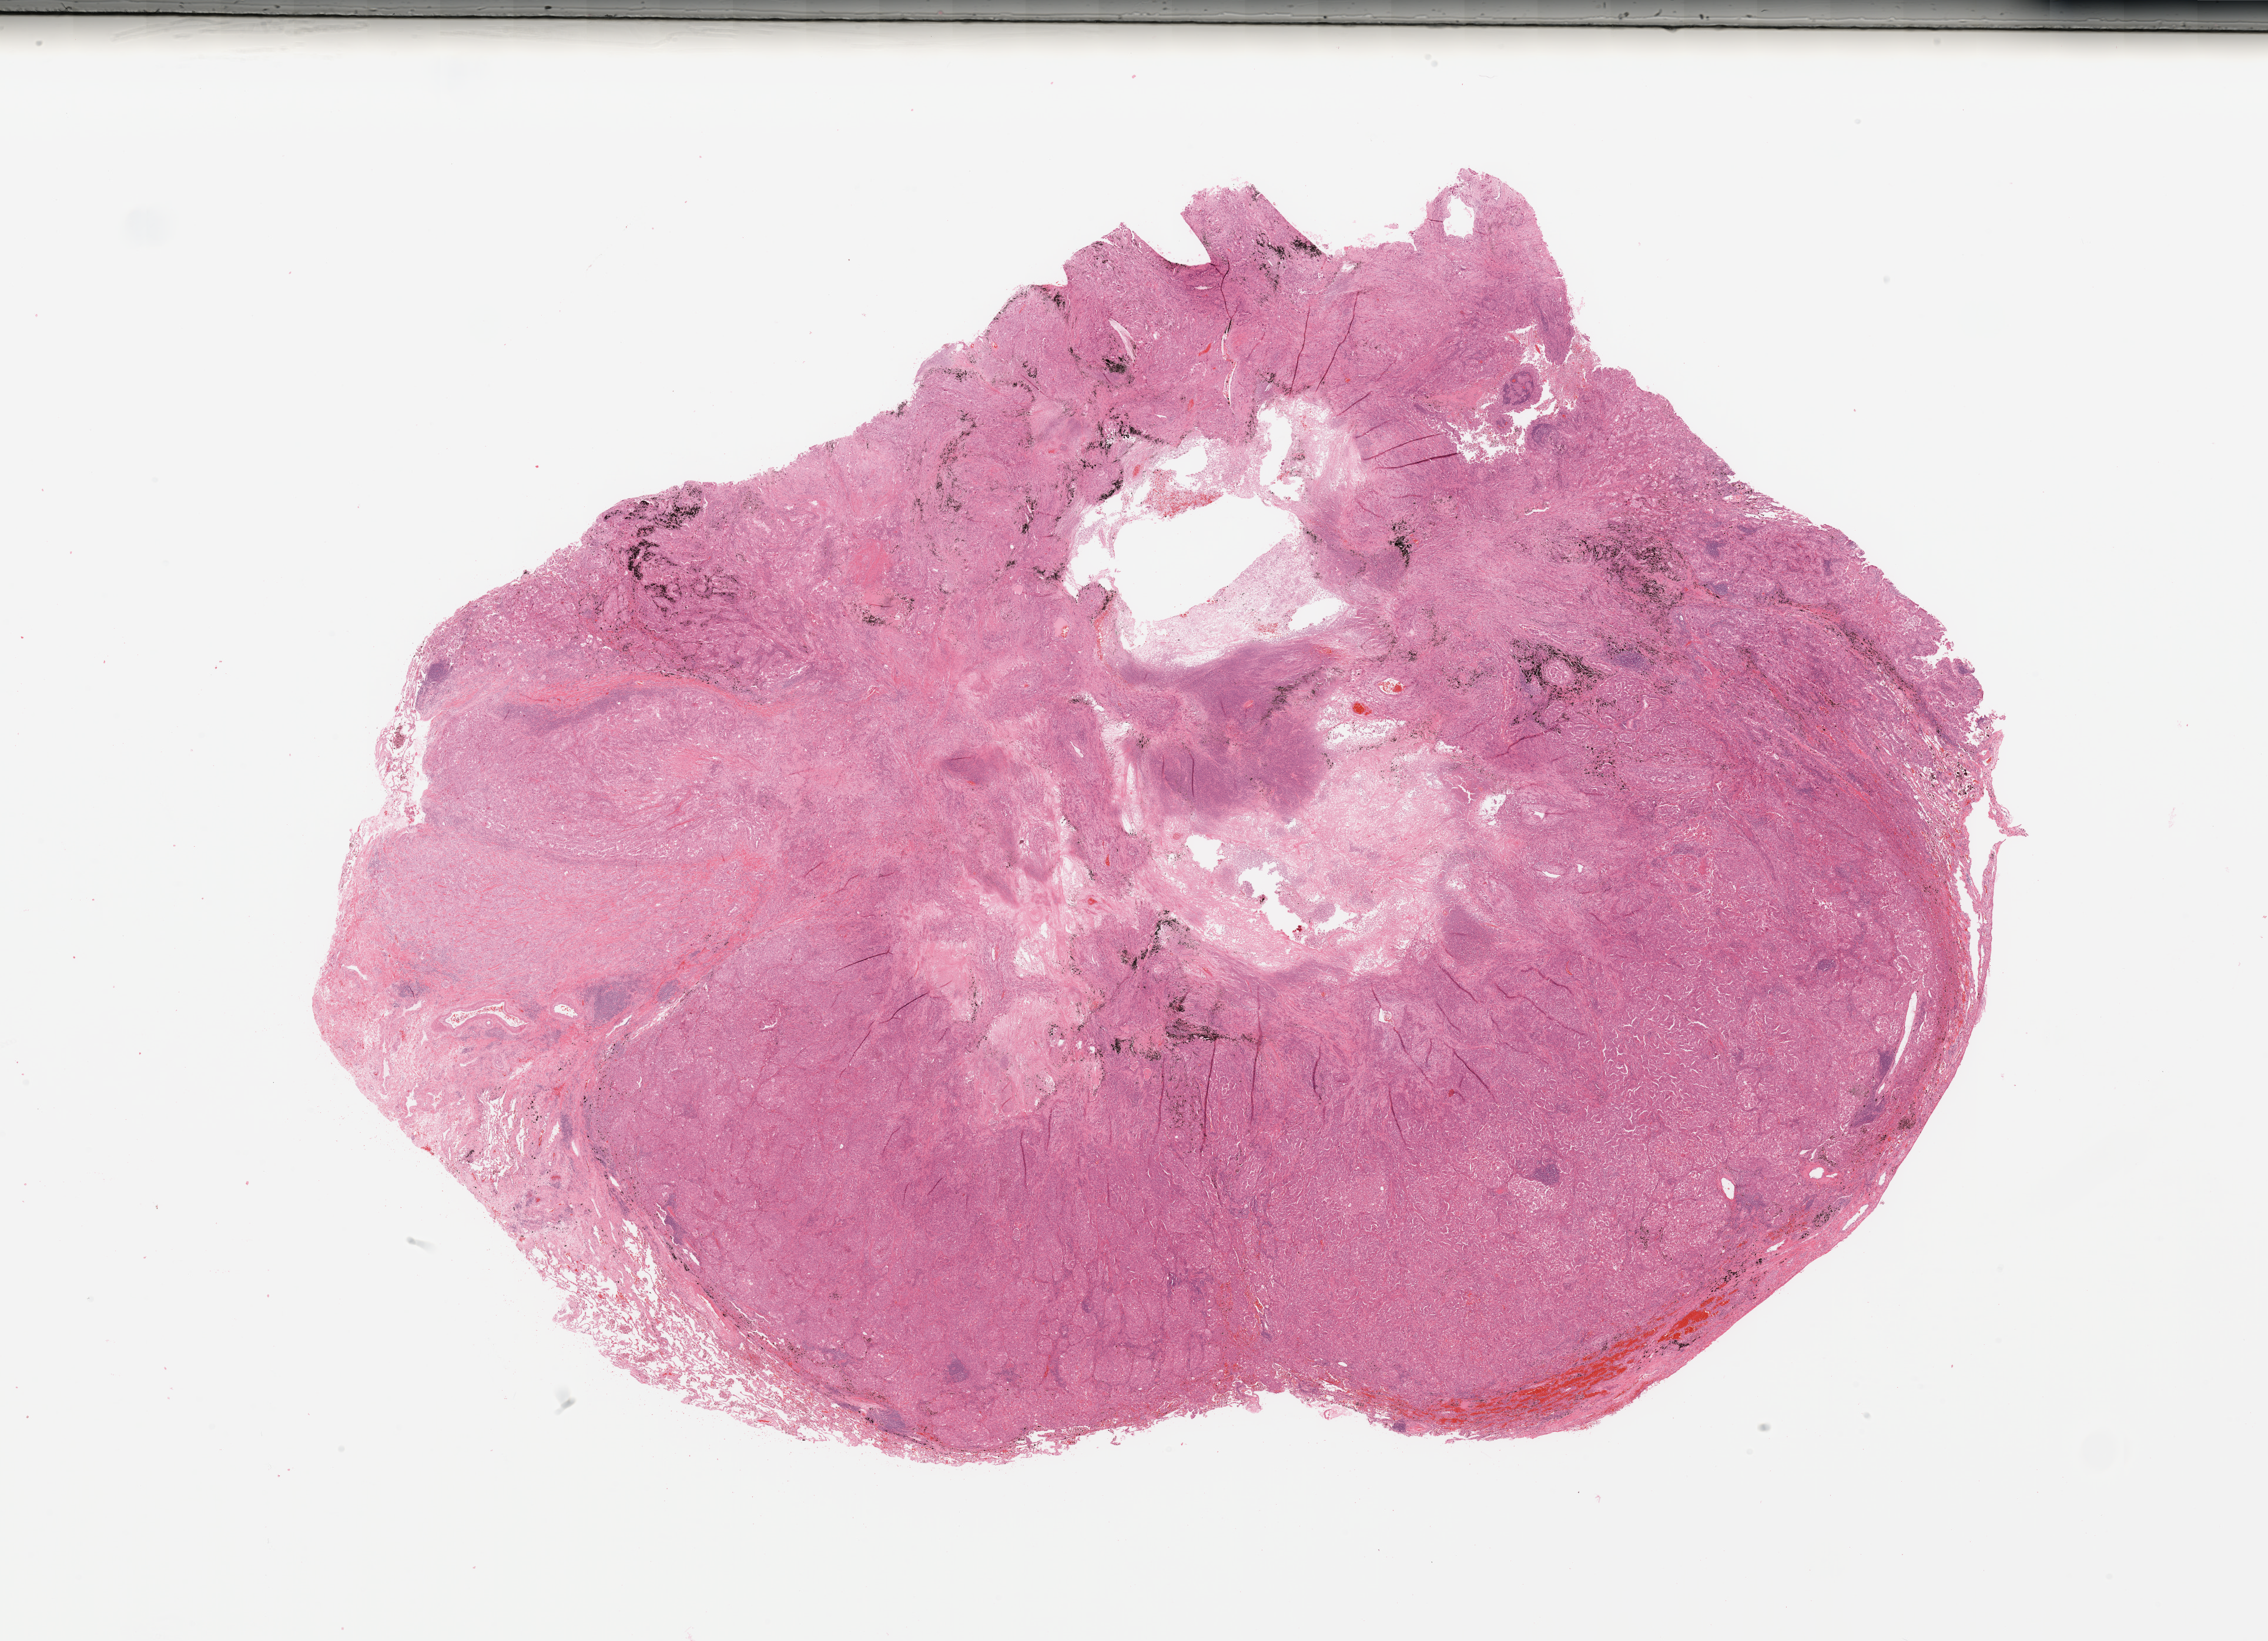
Digitized H&E-stained tissue section (whole slide), shown as a low-resolution overview of the whole scanned area (about 30.5 x 22.1 mm, from a 20x scan). Tumour tissue sample, lung. Male, 71 y/o. Histologic grade: G3 (poorly differentiated).
Diagnosis: Adenocarcinoma, NOS. AJCC pathologic stage: IIIA.